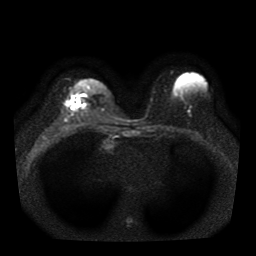
Breast MRI, one axial slice. Slice 23 of 41 in the series (ordered by position). Diffusion-weighted series; image 2 of 4 stored at this slice position (different b-values; order by instance number). 1.5 T. 5 mm slice thickness. 256 × 256 image matrix. Female patient.
Structures marked on this image (outlined manually by an expert reader):
- tumour on diffusion-weighted imaging: bounding box (x1, y1, x2, y2) in pixels: (66, 95, 82, 111)